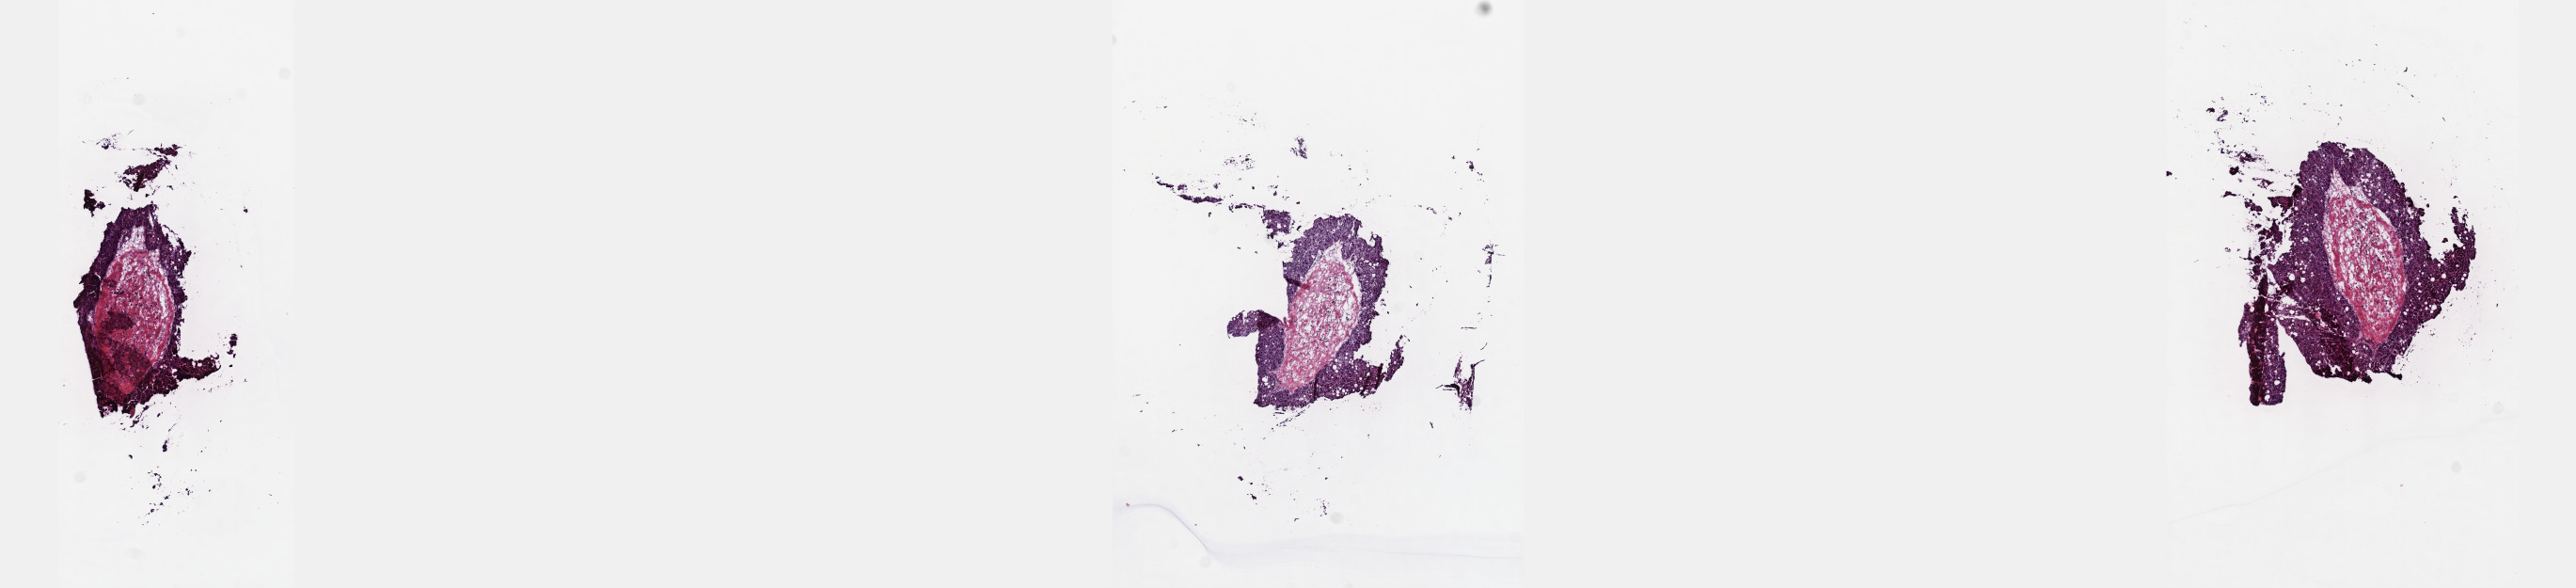
H&E-stained whole-slide image, shown as a low-resolution overview of the whole scanned area (about 22.1 x 5.0 mm, acquisition: 40x scan), frozen section from the top of the tissue portion, sample: primary tumour, liver. Patient: male, age at initial diagnosis 60 years. Histologic grade: G3 (poorly differentiated). Pathologist review of this section (percent, as recorded): tumour cells 40%, tumour nuclei 90%, normal cells 0%, stromal cells 50%, necrosis 10%. Inflammatory infiltration, as recorded: lymphocyte infiltration 0%, monocyte infiltration 0%, neutrophil infiltration 0%.
AJCC pathologic stage: II. Diagnosis: Hepatocellular carcinoma, NOS.